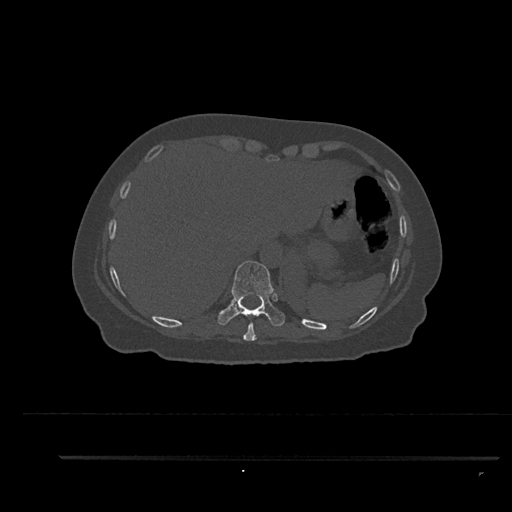
CT including the spine, one axial slice. Slice 373 of 797 in the series (ordered by position). 120 kVp. Bone window (W 1800 / L 400 HU). 512 × 512 image matrix, field of view 408 × 408 mm. Female patient, age 44 years. Case-level facts recorded for this patient, not image findings: primary cancer: renal; vertebrae with lytic lesions (as recorded): L1.
Outlined on this slice (semi-automatic segmentation, software-assisted and operator-edited):
- T10 vertebra: bounding box (x1, y1, x2, y2) in pixels: (218, 260, 285, 331)
- T9 vertebra: (243, 323, 257, 341)